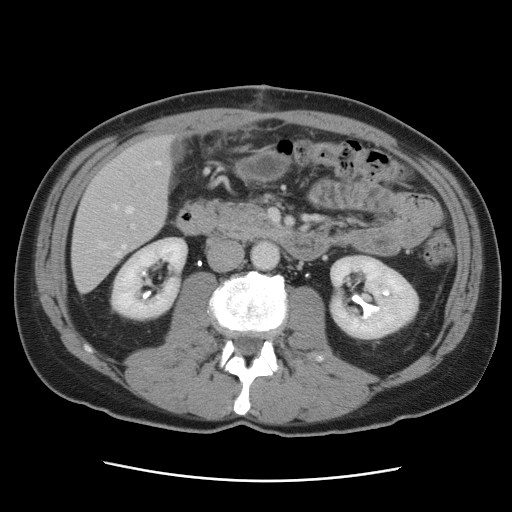
Contrast-enhanced abdominal CT, one axial slice; slice 30 of 89 in the series (ordered by position); intravenous contrast given; soft-tissue window (W 400 / L 40 HU); 5 mm slice thickness; 512 × 512 image matrix, field of view 366 × 366 mm. Male patient, age 59 years. Case-level facts recorded for this patient, not image findings: diagnosis: colorectal cancer liver metastases, imaged before liver resection; multiple liver metastases: yes; largest metastasis: 0.6 cm; disease in both lobes: yes.
Structures marked on this image (outlined manually by an expert reader):
- hepatic veins: bounding box (x1, y1, x2, y2) in pixels: (100, 161, 160, 257)
- liver: (73, 137, 171, 291)
- planned liver remnant (the part of the liver to remain after resection): (74, 137, 172, 246)
- portal vein (with intrahepatic branches): (132, 224, 135, 229)